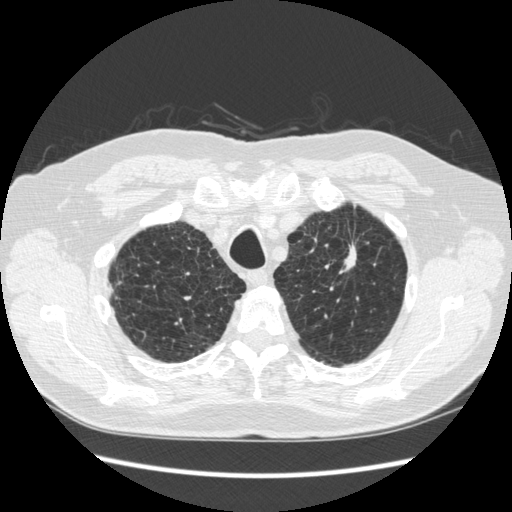
Low-dose screening chest CT, one axial slice; slice 227 of 267 in the series (ordered by position); reconstruction kernel STANDARD; lung window (W 1500 / L -600 HU); 1.25 mm slice thickness; 512 × 512 image matrix, field of view 360 × 360 mm.
Annotated regions visible in this slice (manually delineated by an expert):
- lesion 1 (tumor, upper lobe of left lung): box from (x=342, y=244) to (x=356, y=273) px